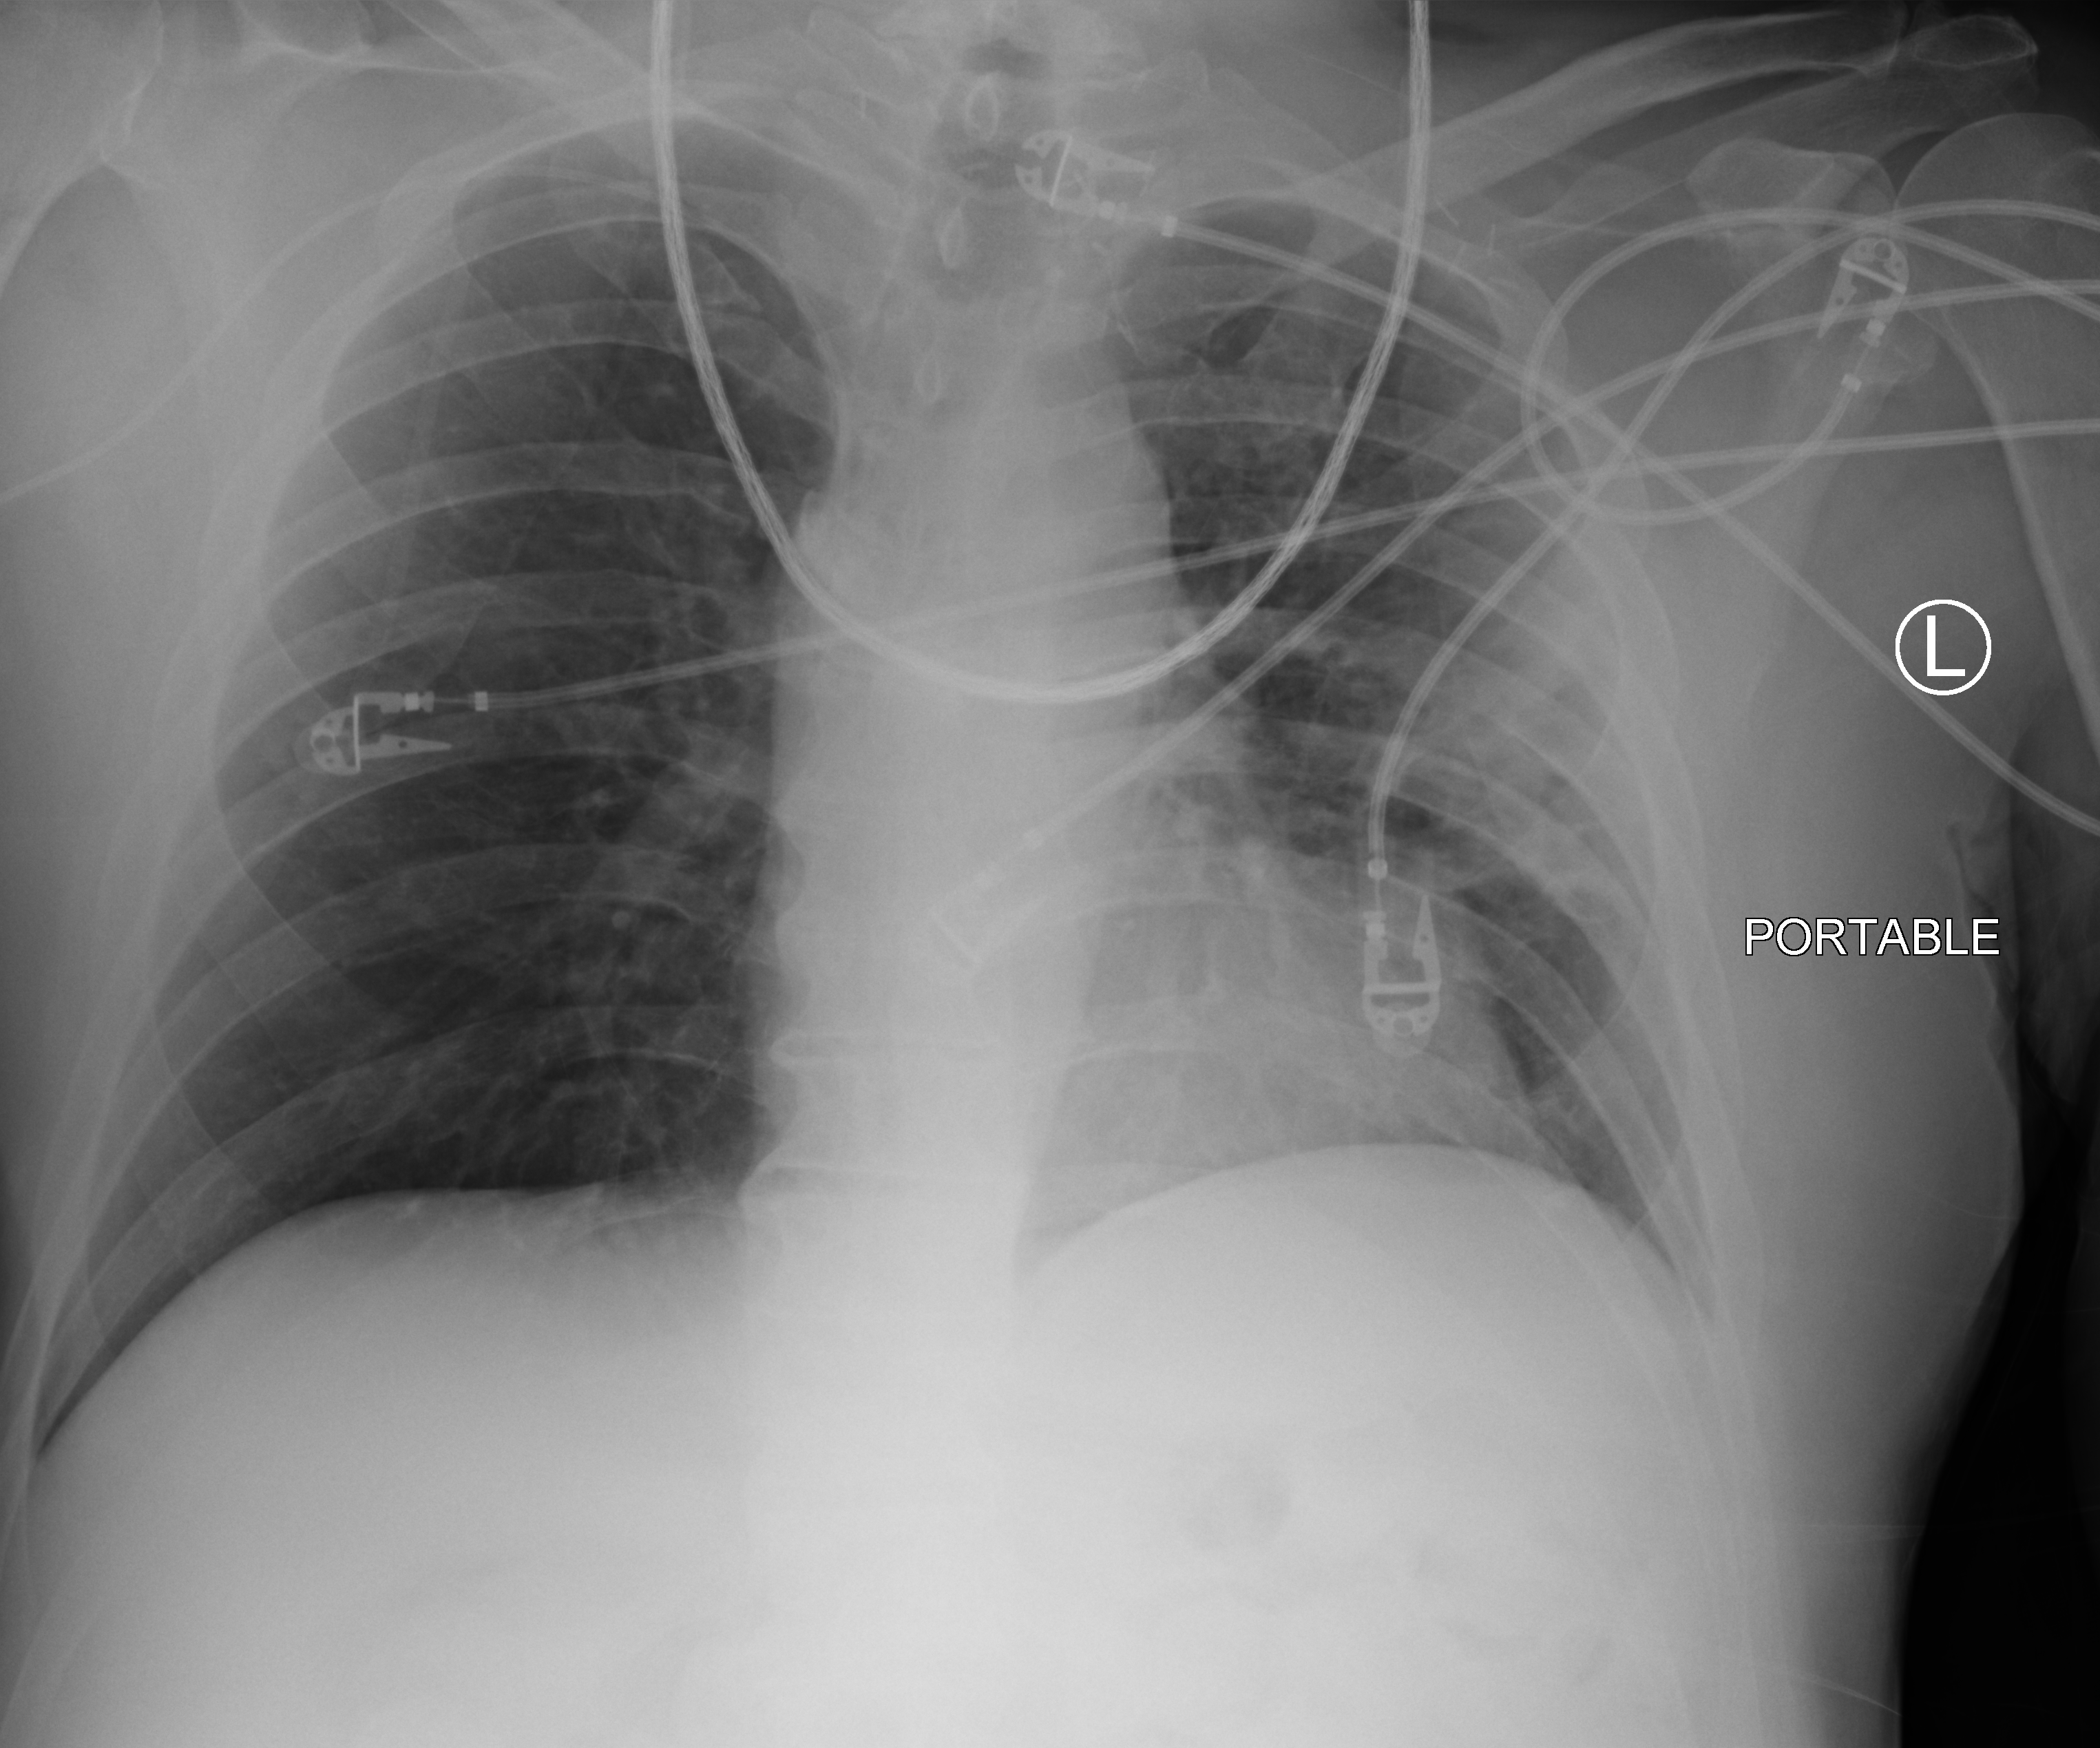
Chest X-ray (portable), anteroposterior (AP) projection. Patient hospitalised with COVID-19, aged 18–59 years.
Hospital-stay facts (about this admission, not read from this image; timing relative to this image not recorded): length of hospital stay: 19 days; smoking status (admission record): never.